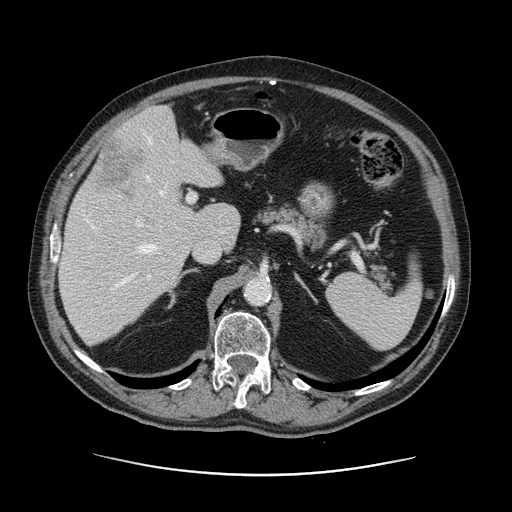
Contrast-enhanced abdominal CT, one axial slice; intravenous contrast given; soft-tissue window (W 400 / L 40 HU); 2.5 mm slice thickness; 512 × 512 image matrix, field of view 395 × 395 mm. Male patient, age 72 years. From the clinical record (not read from this slice): diagnosis: colorectal cancer liver metastases, imaged before liver resection; multiple liver metastases: yes; largest metastasis: 5.4 cm; chemotherapy before resection: yes.
Annotated regions visible in this slice (manually delineated by an expert):
- hepatic veins: box from (x=97, y=132) to (x=167, y=302) px
- liver: (x=59, y=106)–(x=240, y=345)
- planned liver remnant (the part of the liver to remain after resection): (x=59, y=140)–(x=240, y=345)
- portal vein (with intrahepatic branches): (x=85, y=193)–(x=197, y=290)
- liver metastasis: (x=96, y=141)–(x=144, y=199)